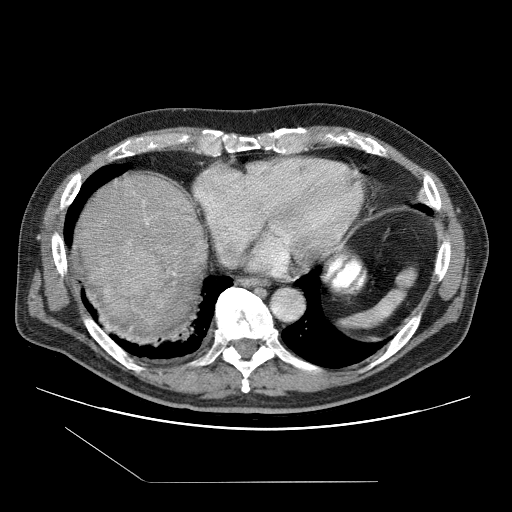
Contrast-enhanced abdominal CT (liver protocol), one axial slice; position 94 of 109 along the scan axis; 120 kVp; one of 2 acquisitions stored at this slice position; soft-tissue window (W 400 / L 40 HU); 2.5 mm slice thickness; 512 × 512 image matrix. From the clinical record (not read from this slice): diagnosis: hepatocellular carcinoma (patient treated with transarterial chemoembolisation; whether this scan precedes or follows treatment is not stated here); TNM stage (as recorded): Stage-IIIB; Child-Pugh class: A; tumour differentiation: well differentiated; tumour nodularity: multinodular.
Structures marked on this image (semi-automatically segmented with operator editing):
- liver parenchyma outside the tumour (the mass and vessels are separate outlines, so this box may not span the whole liver): bounding box [x1, y1, x2, y2] px = [74, 174, 206, 337]
- mass: [92, 240, 163, 318]
- liver vessels: [146, 222, 175, 275]